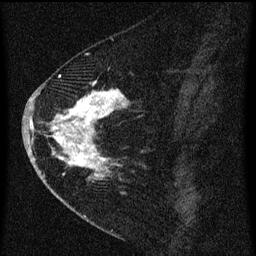
Breast MRI (dynamic contrast-enhanced), one sagittal slice. Dynamic contrast-enhanced series, image 2 of 3 at this slice position (ordered by acquisition). 1.5 T. TE 4.2 ms, TR 8 ms. 2 mm slice thickness. 256 × 256 image matrix, field of view 180 × 180 mm. Female patient, age 47 years.
Structures marked on this image (semi-automatic segmentation, software-assisted and operator-edited):
- analysis volume of interest (the breast-tissue region the enhancement analysis was run in; not a lesion): bounding box (x1, y1, x2, y2) in pixels: (38, 76, 144, 193)
- tumour enhancement mask (voxels above the 70 % enhancement threshold inside the analysis volume of interest): (51, 76, 128, 181)